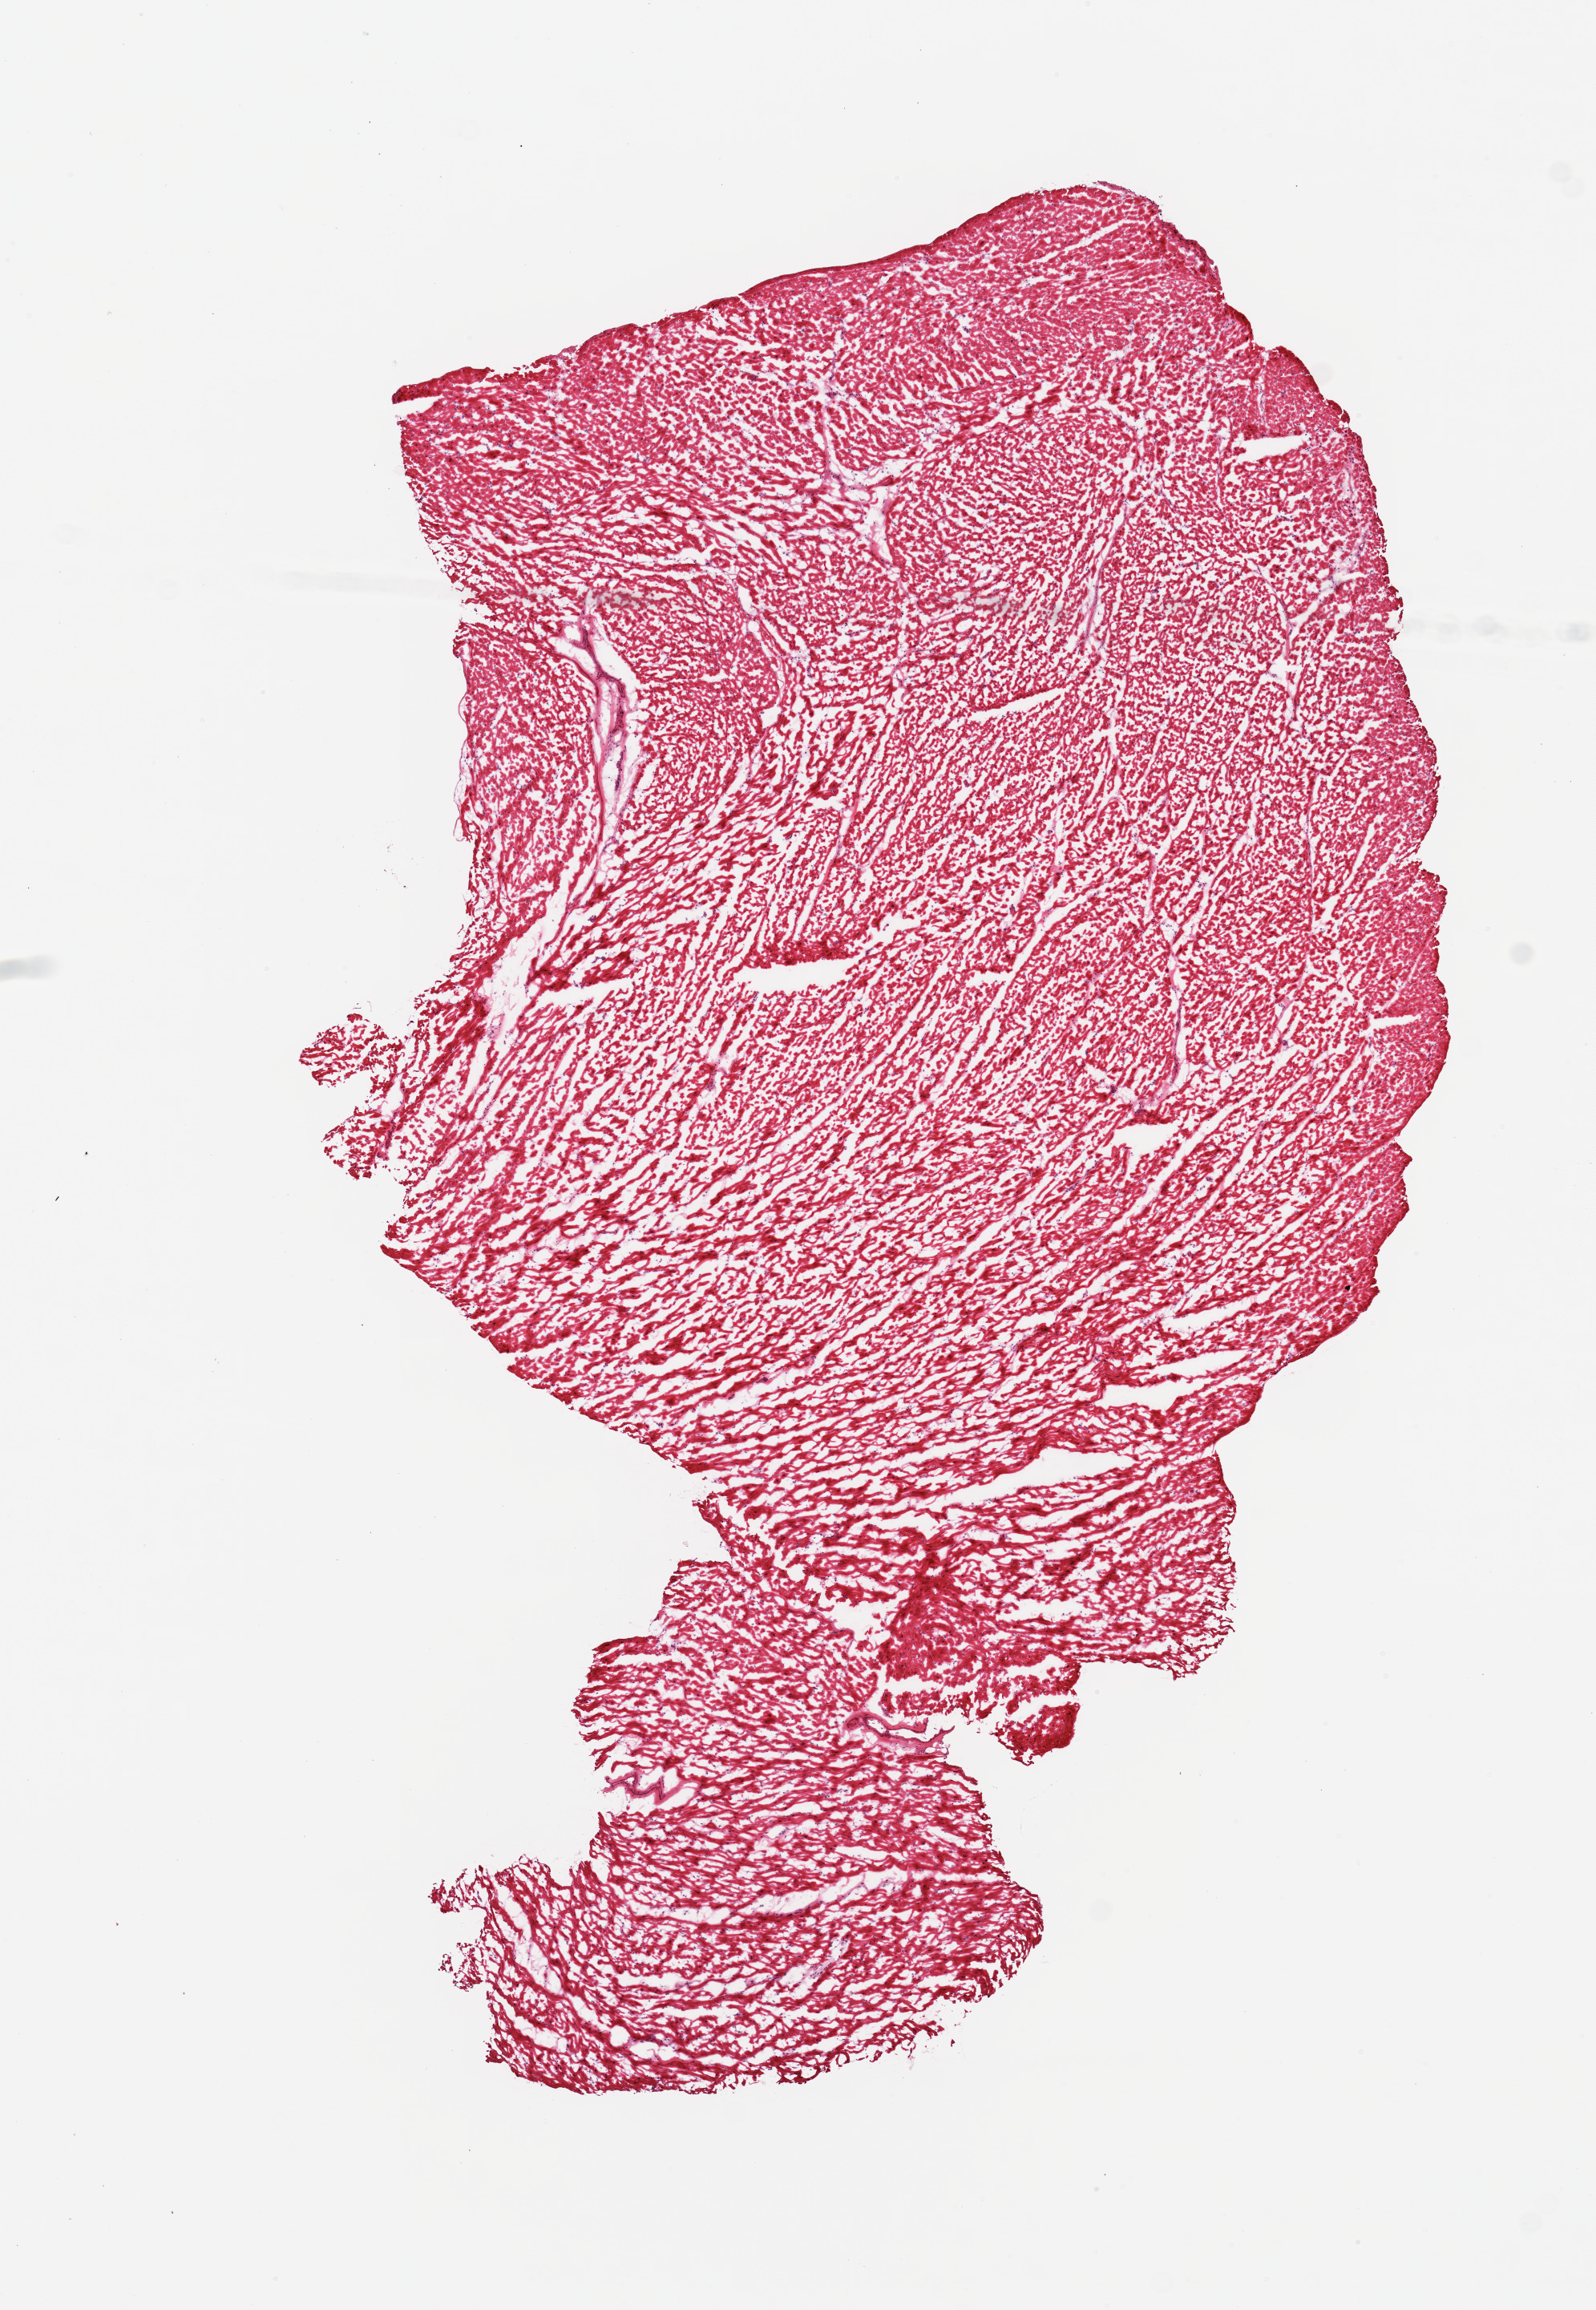
H&E whole-slide image, a low-resolution overview of the entire scanned area, about 7.9 x 11.4 mm; frozen section; sampled site (target tissue): heart; donor tissue sample. Donor sex: male.
Review note (as recorded): 1 piece.